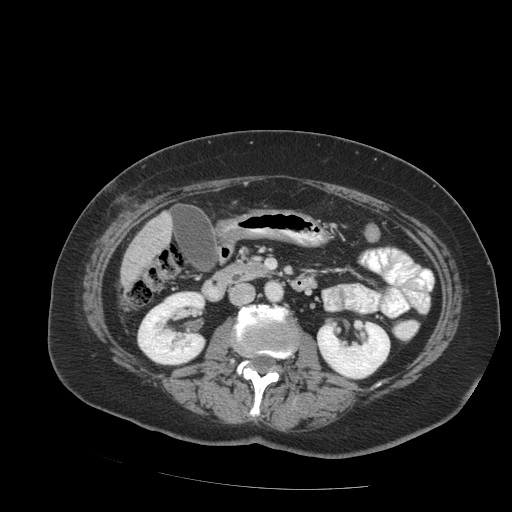
Contrast-enhanced abdominal CT (liver protocol), one axial slice. Slice 27 of 99 in the series (ordered by position). 140 kVp. Soft-tissue window (W 400 / L 40 HU). 2.5 mm slice thickness. 512 × 512 image matrix, field of view 400 × 400 mm. Case-level facts recorded for this patient, not image findings: diagnosis: hepatocellular carcinoma (patient treated with transarterial chemoembolisation; whether this scan precedes or follows treatment is not stated here); TNM stage (as recorded): Stage-IVB; Child-Pugh class: A.
Structures marked on this image (semi-automatic segmentation, software-assisted and operator-edited):
- liver parenchyma outside the tumour (the mass and vessels are separate outlines, so this box may not span the whole liver): bounding box <120,212,172,289> (left, top, right, bottom; pixels)